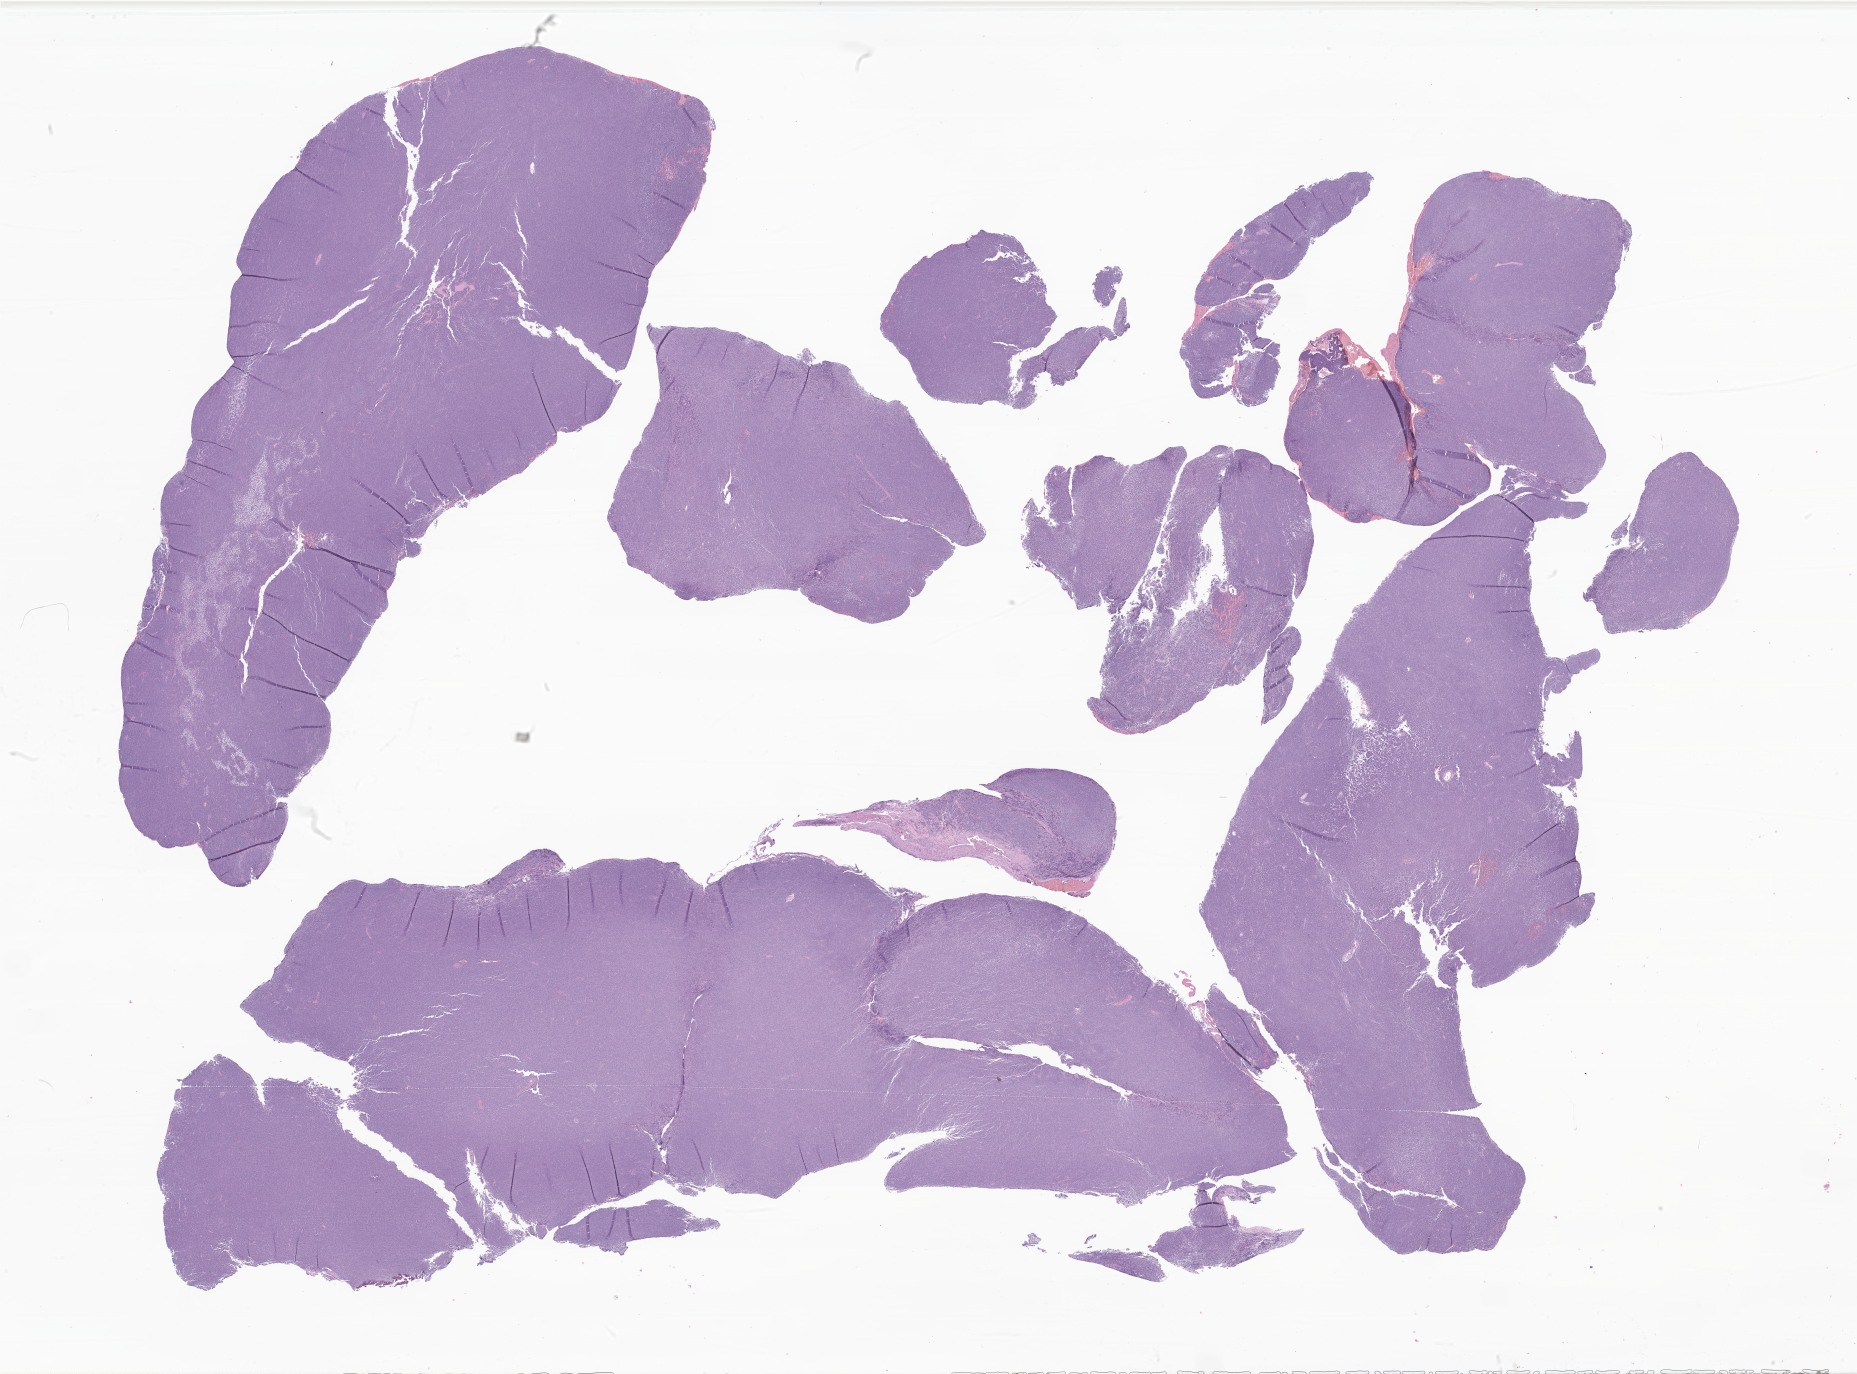
Digitized haematoxylin and eosin-stained section of tumor tissue from the brain, low-resolution overview of the scanned area, about 31.3 x 23.2 mm, FFPE section. Male patient, age 177 months (14 years 9 months).
• diagnosis: Medulloblastoma, NOS